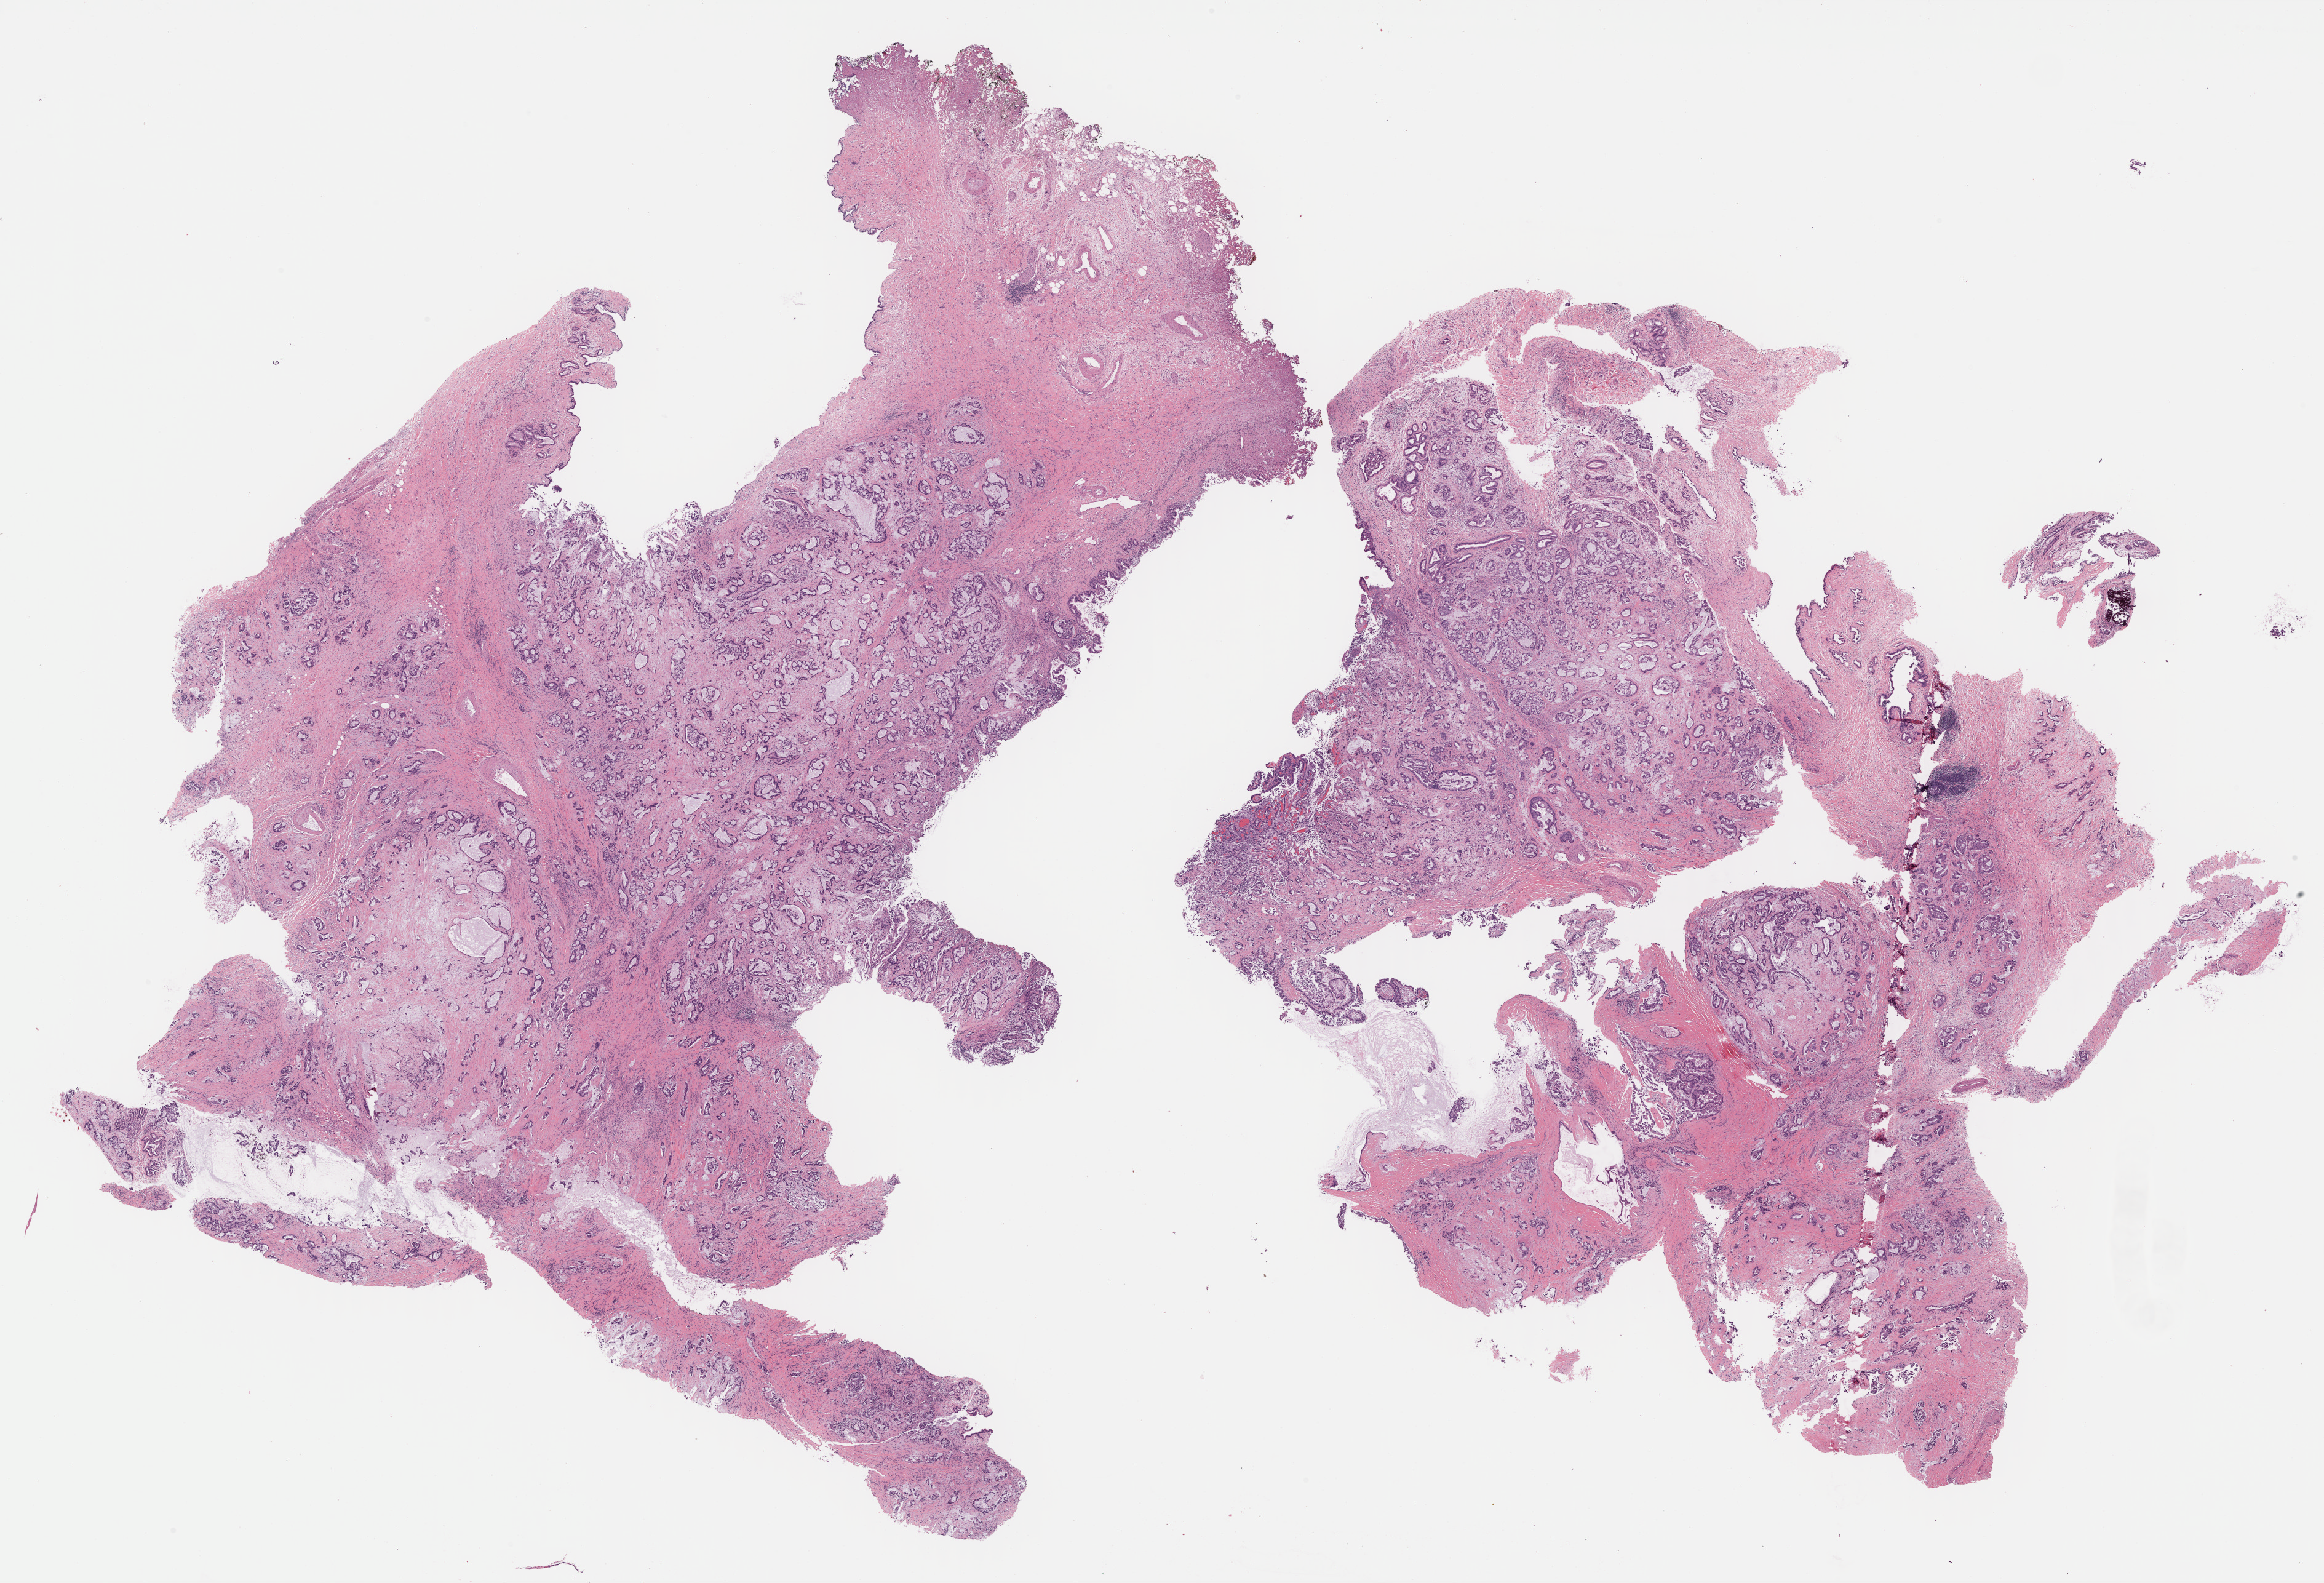
Whole-slide histology image, H&E, a low-resolution overview of the entire scanned area, about 30.6 x 20.8 mm, FFPE section, bile duct, primary tumour sample. Male patient; age at initial diagnosis 67 years. Histologic grade: G4 (undifferentiated).
* TNM: T2b N1 M1
* histologic diagnosis: Cholangiocarcinoma (extrahepatic bile duct)
* AJCC pathologic stage: IVB